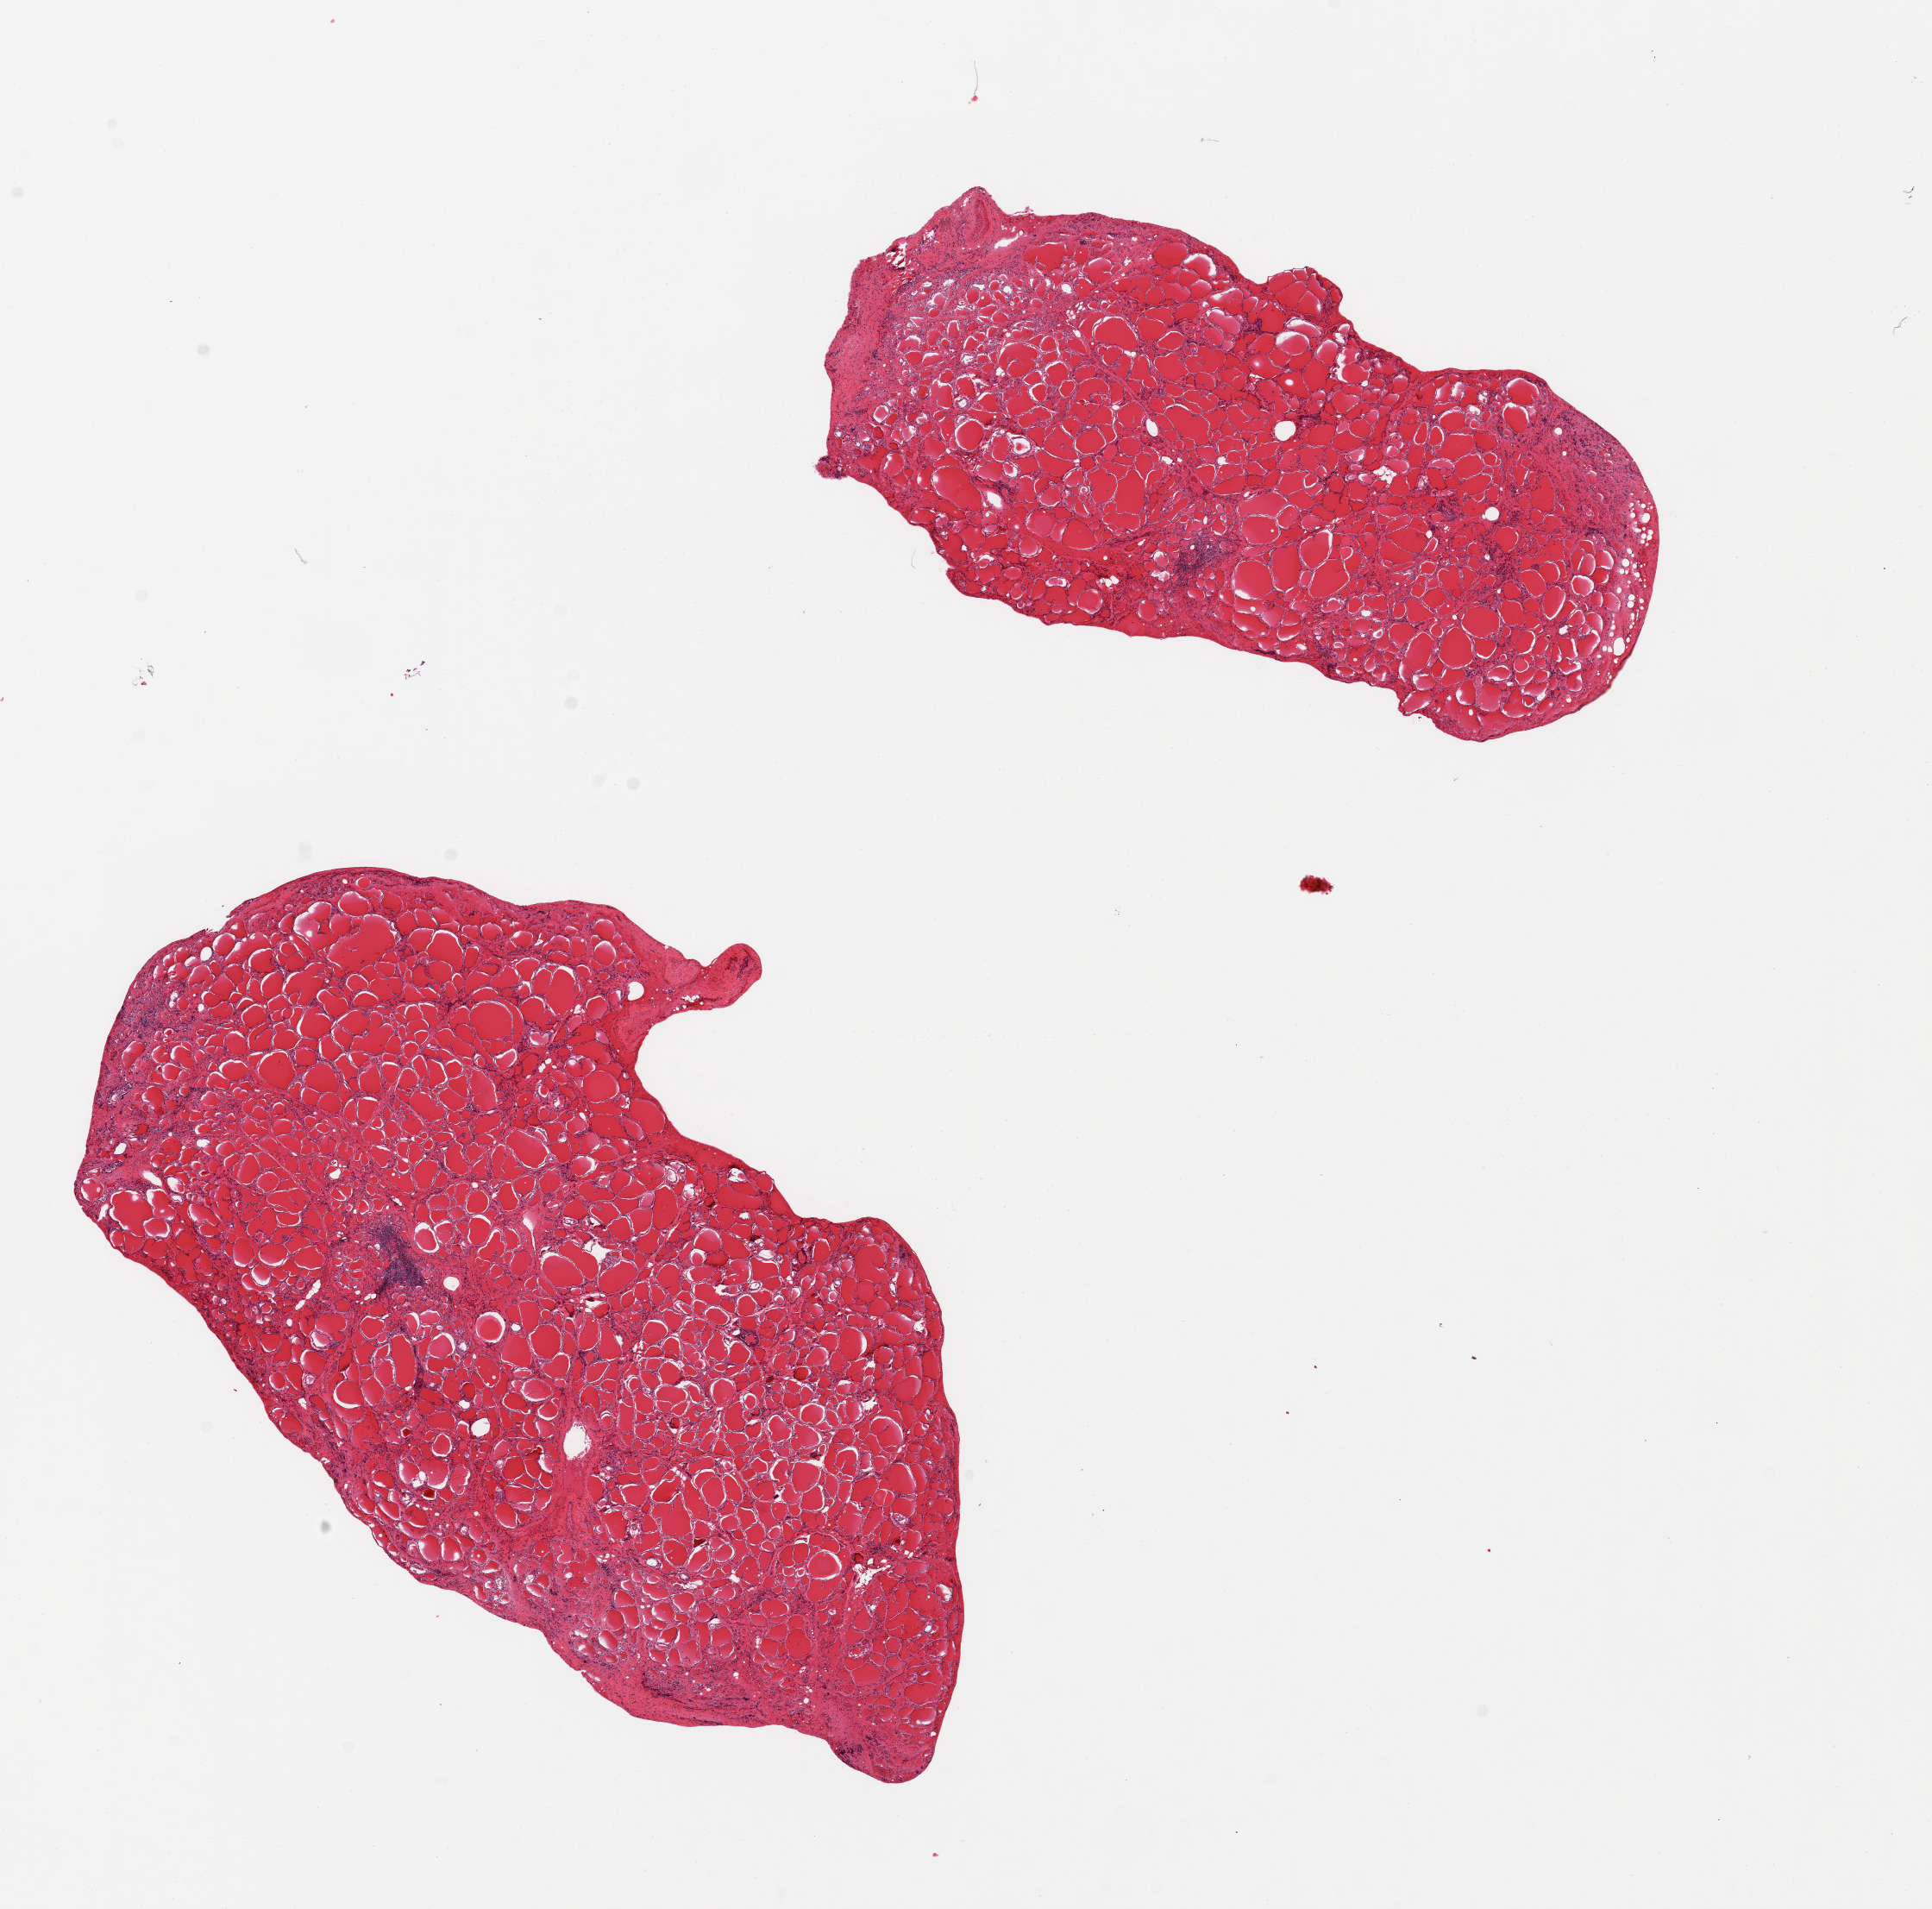
Whole-slide image, hematoxylin and eosin (H&E) stain, shown as a low-resolution overview of the whole scanned area (about 17.7 x 17.5 mm, slide scanned at 20x). PAXgene-fixed paraffin-embedded (PFPE) section. Section of thyroid (target tissue). Tissue donor sample. Donor: male.
• reviewer comment on this tissue sample: 2 pieces, patchy lymphocytic thyroiditis, Hashimoto--type